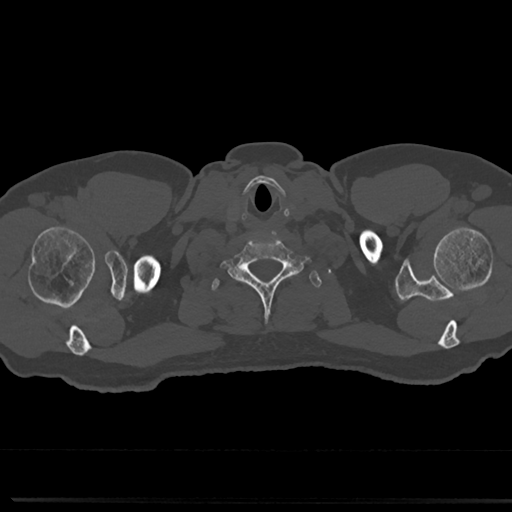
CT including the spine, one axial slice. Position 701 of 817 along the scan axis. 120 kVp. Bone window (W 1800 / L 400 HU). 512 × 512 image matrix. Patient: male, 61 years. From the clinical record (not read from this slice): primary cancer: prostate.
Annotated regions visible in this slice (semi-automatic segmentation, software-assisted and operator-edited):
- T1 vertebra: bounding box <209,270,319,296> (left, top, right, bottom; pixels)